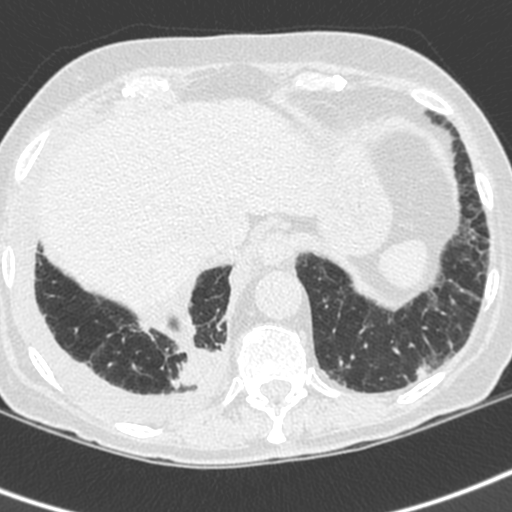
Low-dose screening chest CT, axial slice; first (baseline) screen; lung window (W 1500 / L -600 HU); 1.3 mm slice thickness; standard (soft-tissue) reconstruction kernel (C); 120 kVp; slice 157 of 192 in the series. Female, age 73 years at enrolment. Current smoker at enrolment.
Expert reader's lesion annotation, bounding box (x1, y1, x2, y2) in pixels: (161, 327, 235, 405). The exam's reader record, not a measurement of the box and not confirmed to be the same lesion: non-calcified nodule or mass ≥4 mm, right lower lobe, 35 × 30 mm, spiculated (stellate) margins, soft tissue attenuation. Later outcome: lung cancer diagnosed 22 days after this screen — adenocarcinoma, NOS, right lower lobe, stage IV (AJCC 6th edition), 35 mm at pathology.